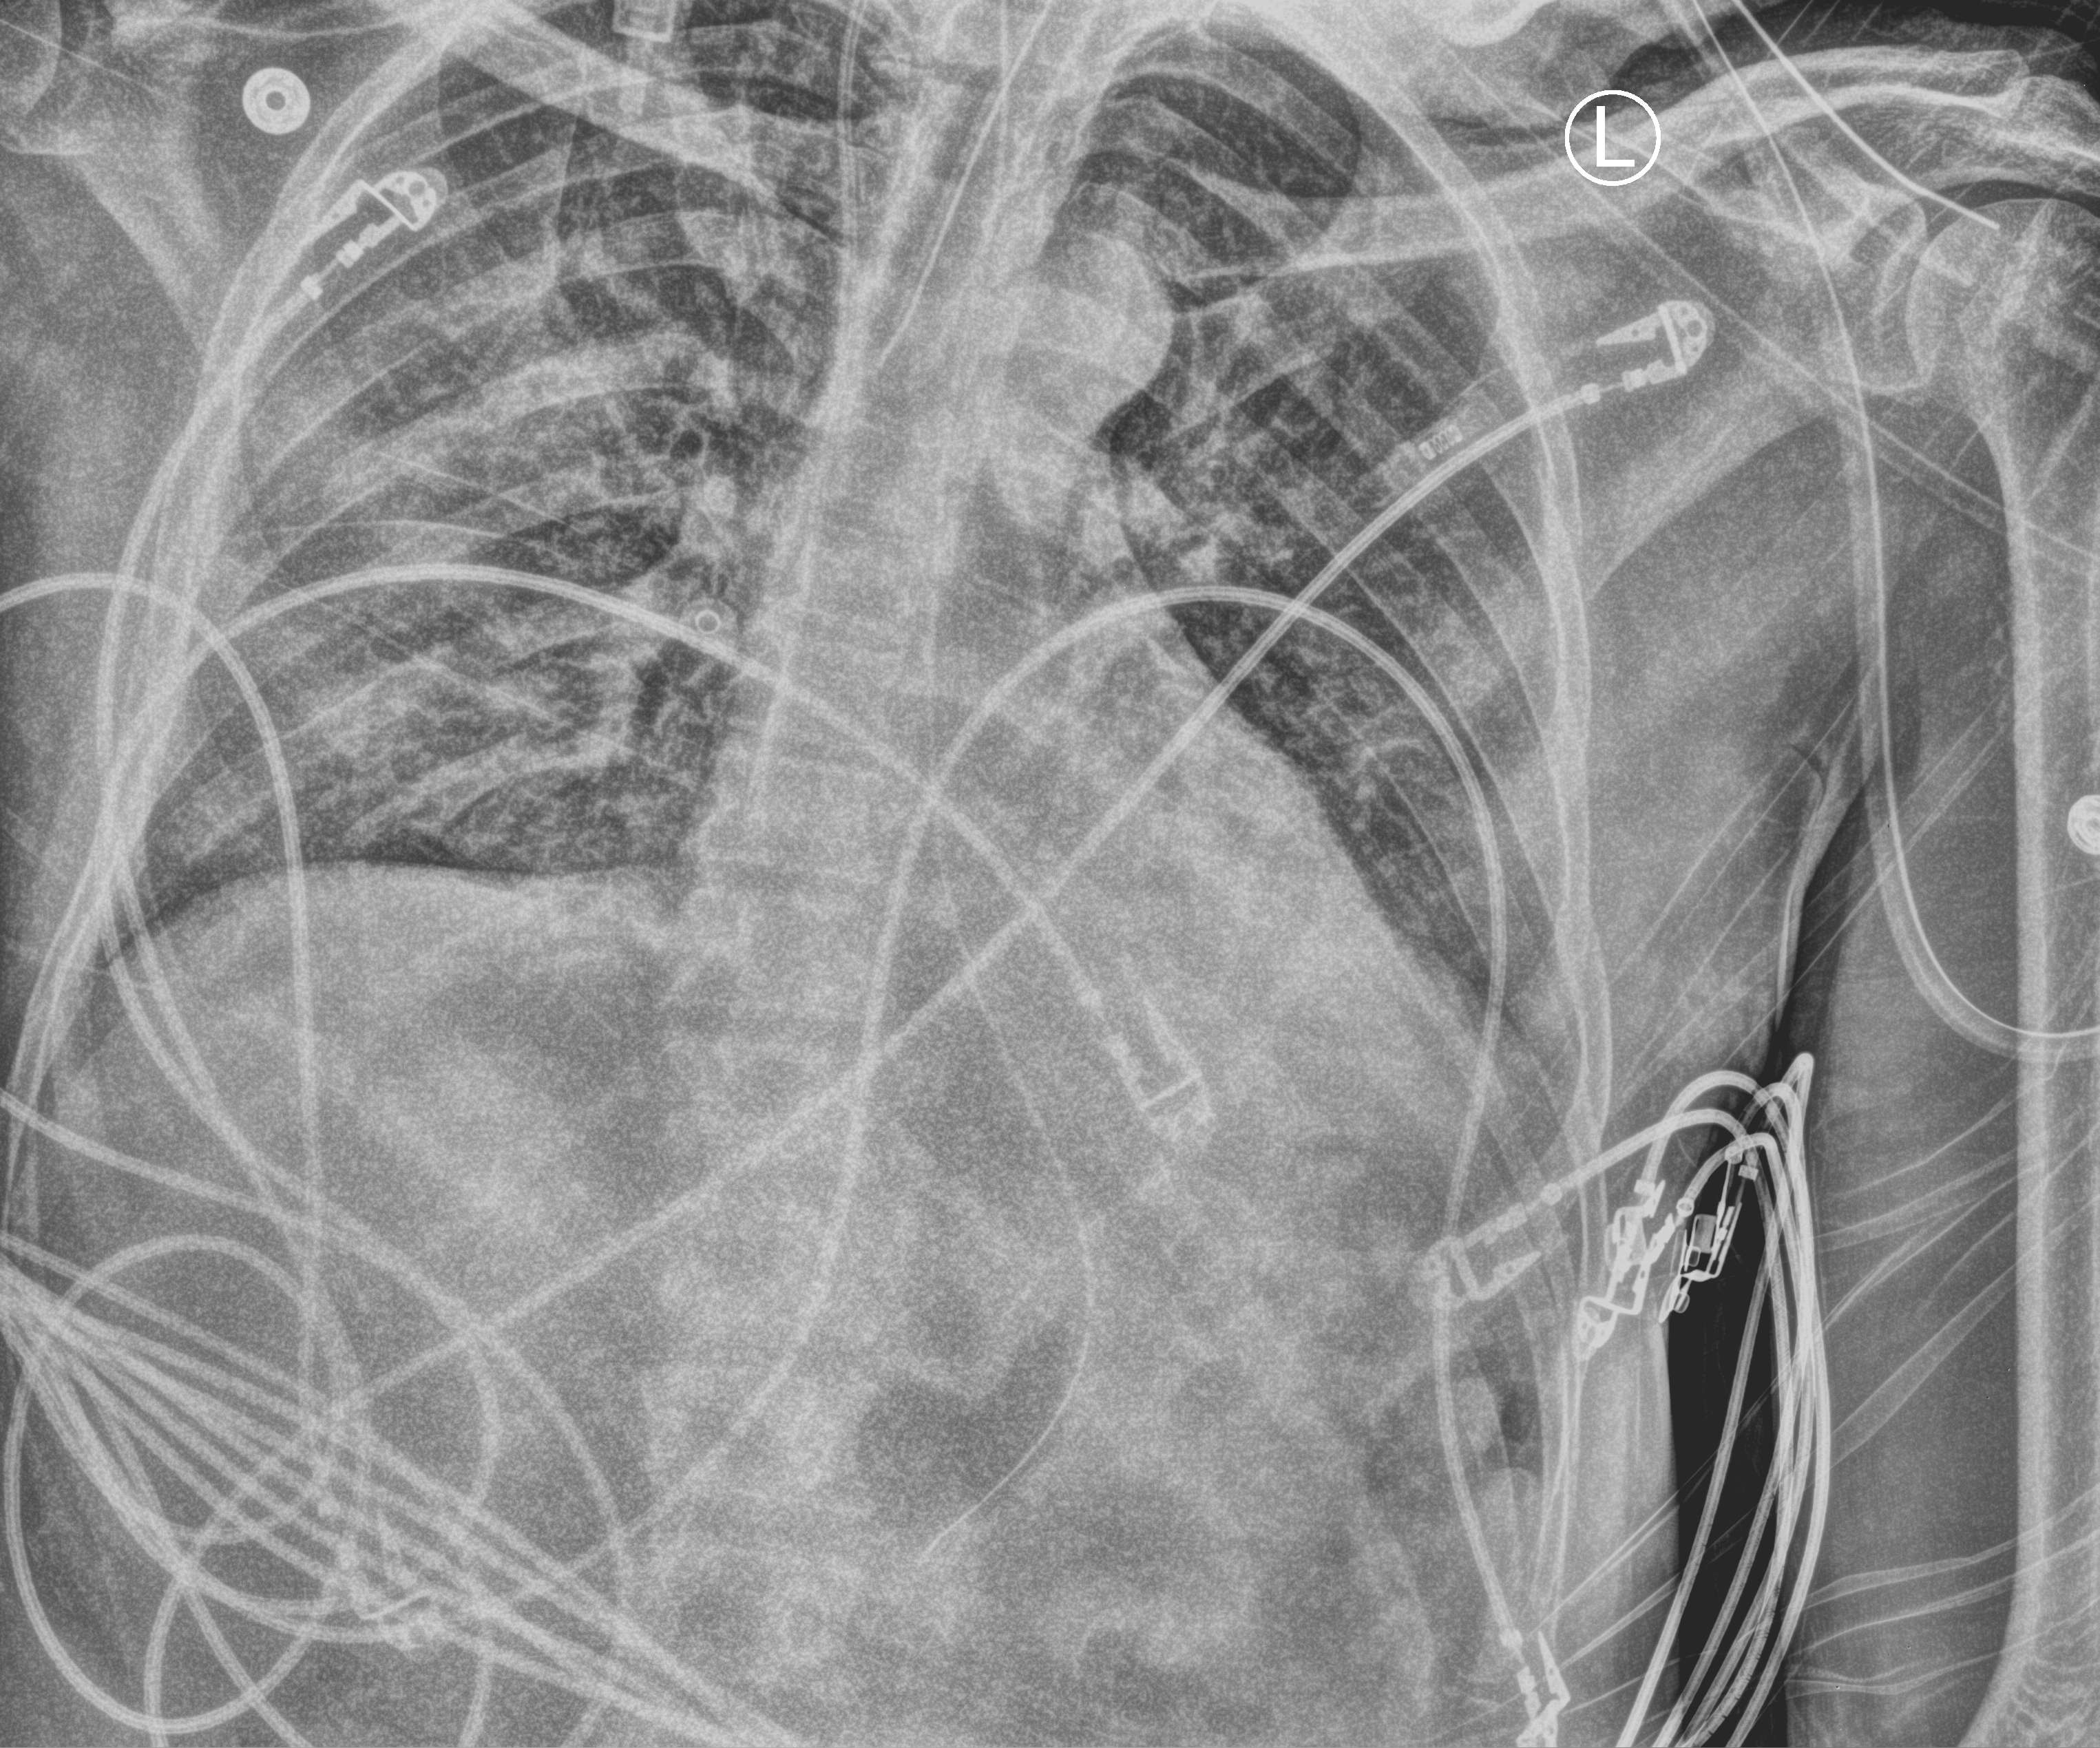
Portable chest radiograph, anteroposterior (AP) projection. Male patient hospitalised with COVID-19, age 18–59 years.
Hospital-stay facts (about this admission, not read from this image; timing relative to this image not recorded): smoking status (admission record): never; length of hospital stay: 41 days.